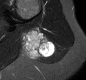
MRI of an extremity soft-tissue mass, one axial slice; slice 15 of 30 in the series (ordered by position); STIR; MR volume resampled by the dataset authors to the PET/CT grid (not the native acquisition matrix); 3.27 mm slice thickness; 86 × 80 image matrix, field of view 84 × 78 mm. Female patient. Case-level facts recorded for this patient, not image findings: histological type: malignant fibrous histiocytoma; grade: low; site of the primary tumour: left arm.
Annotated regions visible in this slice (expert contour drawn on MRI and transferred to this co-registered scan by the dataset authors):
- gross tumour volume (mass): box from (x=20, y=28) to (x=55, y=59) px